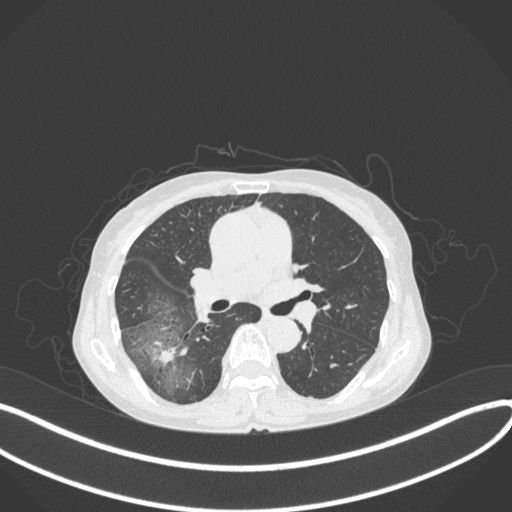
Chest CT, one axial slice. Slice 227 of 379 in the series (ordered by position). 120 kVp. Lung window (W 1500 / L -600 HU). 1 mm slice thickness. 512 × 512 image matrix. Patient: female, 69 years. Case-level facts recorded for this patient, not image findings: clinical TNM (as recorded): T1b N0 M0; histopathological grade: G2-3.
Annotated regions visible in this slice (bounding box drawn by a radiologist):
- lung tumour (recorded histology: adenocarcinoma): bounding box [x1, y1, x2, y2] px = [150, 339, 181, 371]